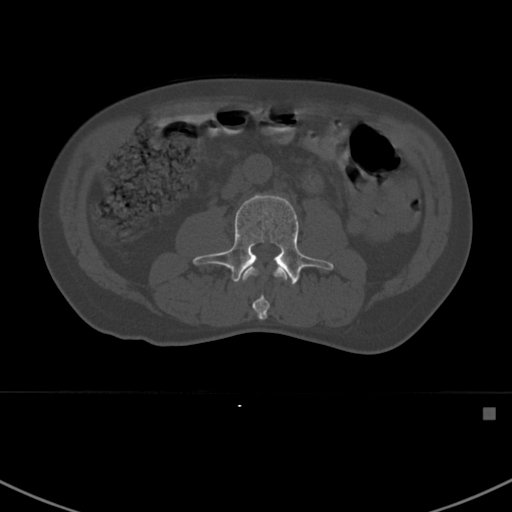
CT including the spine, one axial slice. Position 268 of 412 along the scan axis. 120 kVp. Bone window (W 1800 / L 400 HU). 1.5 mm slice thickness. 512 × 512 image matrix, field of view 358 × 358 mm. Male patient, age 59 years. Case-level facts recorded for this patient, not image findings: primary cancer: prostate.
Annotated regions visible in this slice (semi-automatic segmentation, software-assisted and operator-edited):
- L2 vertebra: bounding box (x1, y1, x2, y2) in pixels: (242, 266, 289, 320)
- L3 vertebra: (191, 194, 334, 285)